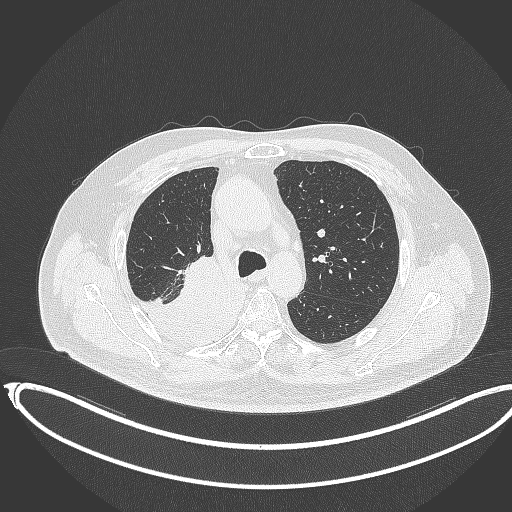
Chest CT, one axial slice; lung window (W 1500 / L -600 HU); 1 mm slice thickness; 512 × 512 image matrix, field of view 436 × 436 mm. Patient: male, 68 years. Case-level facts recorded for this patient, not image findings: clinical TNM (as recorded): T2a N0 M0.
Annotated regions visible in this slice (bounding box drawn by a radiologist):
- lung tumour (recorded histology: adenocarcinoma): bounding box <129,250,254,350> (left, top, right, bottom; pixels)